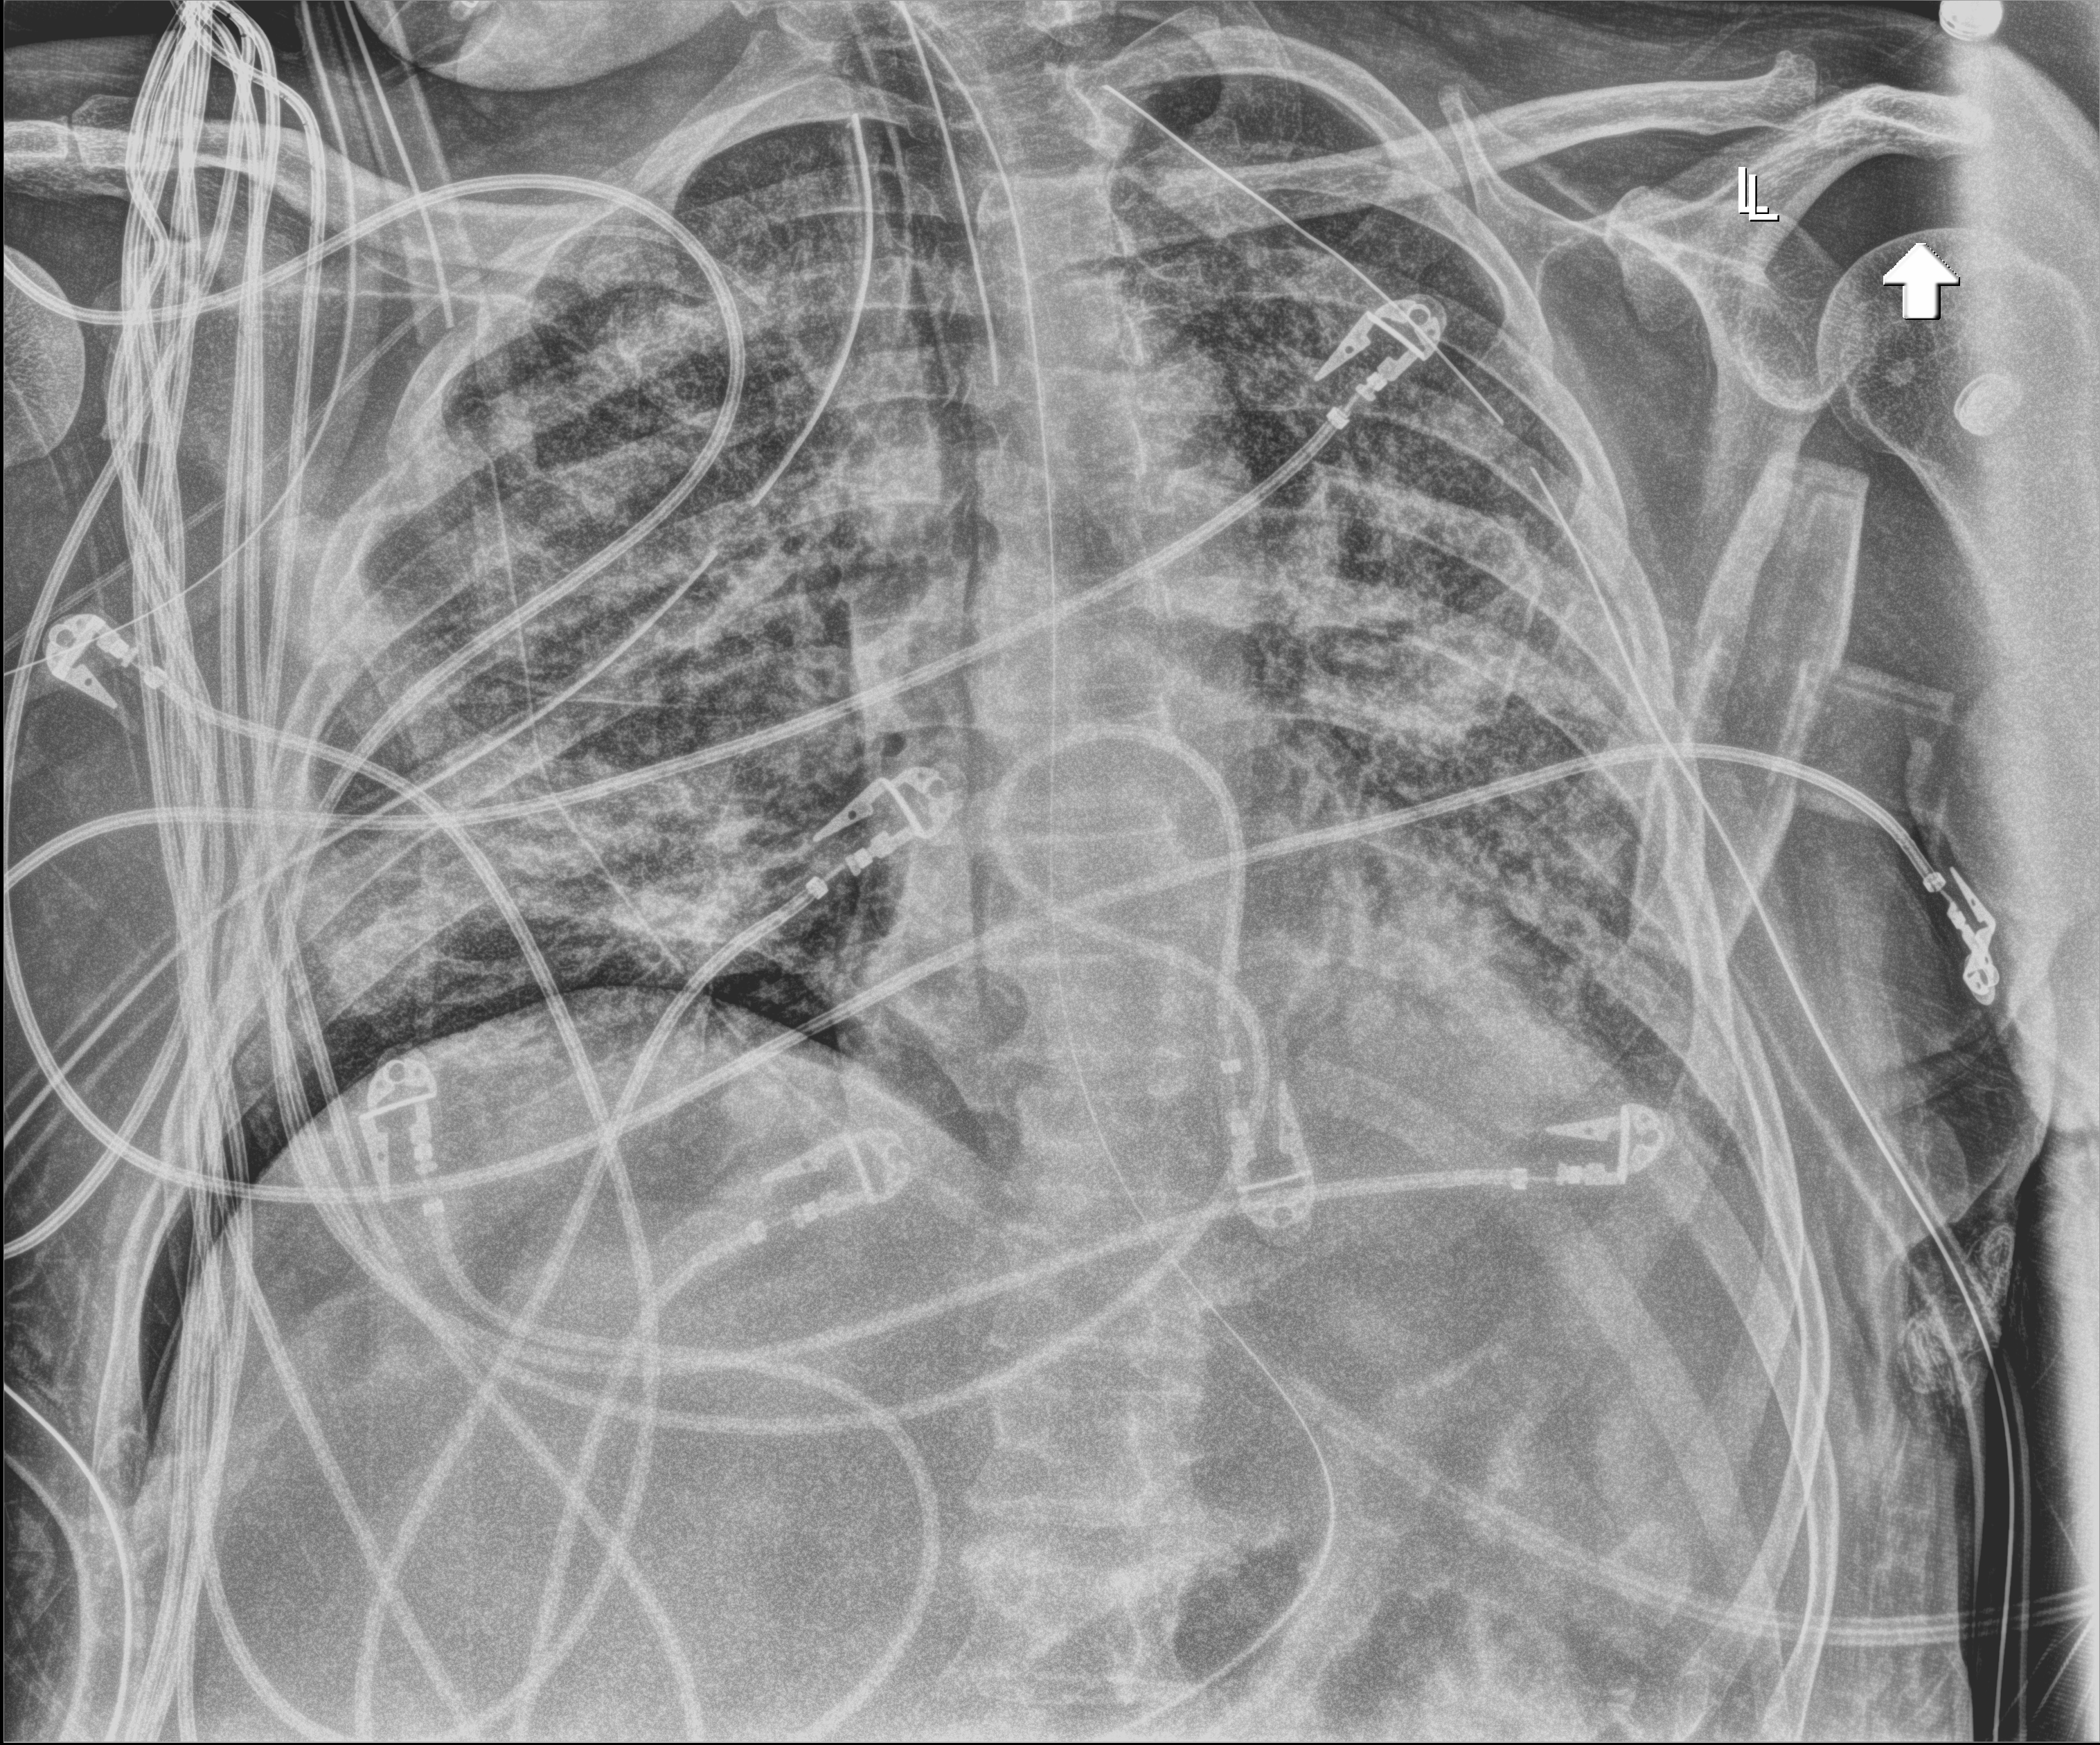
Portable chest radiograph. Male patient hospitalised with COVID-19, age 18–59 years.
Hospital-stay facts (about this admission, not read from this image; timing relative to this image not recorded): admitted to intensive care during this hospital stay: yes; mechanically ventilated during this hospital stay: yes.